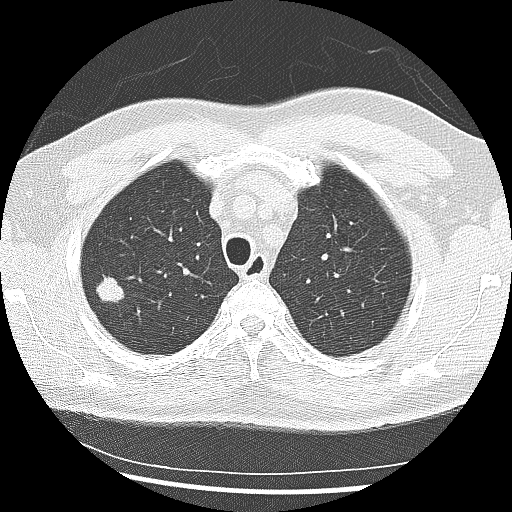
Low-dose screening chest CT, one axial slice. Slice 210 of 265 in the series (ordered by position). Reconstruction kernel LUNG. Lung window (W 1500 / L -600 HU). 2.5 mm slice thickness. 512 × 512 image matrix.
Outlined on this slice (expert manual segmentation):
- lesion 1 (tumor, upper lobe of right lung): box from (x=96, y=276) to (x=125, y=303) px